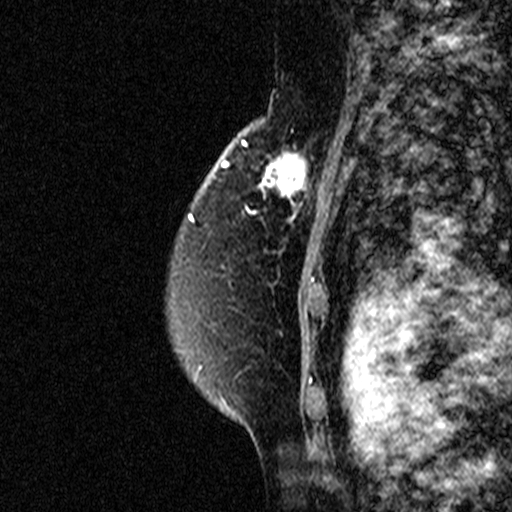
Breast MRI (dynamic contrast-enhanced), one sagittal slice. Position 31 of 44 along the scan axis. Dynamic contrast-enhanced study with each time point stored as its own series, time point 2 of 3 at this slice position (early post-contrast, ordered by acquisition time). 1.5 T. TE 4.5 ms, TR 11 ms. 3 mm slice thickness. 512 × 512 image matrix. Patient: female, 49 years. Case-level facts recorded for this patient, not image findings: setting: breast cancer imaged before/during neoadjuvant chemotherapy; receptor status: triple-negative.
Outlined on this slice (semi-automatic segmentation, software-assisted and operator-edited):
- analysis volume of interest (the breast-tissue region the enhancement analysis was run in; not a lesion): bounding box <253,122,331,227> (left, top, right, bottom; pixels)
- tumour enhancement mask (voxels above the 90 % enhancement threshold inside the analysis volume of interest): <261,150,313,215>